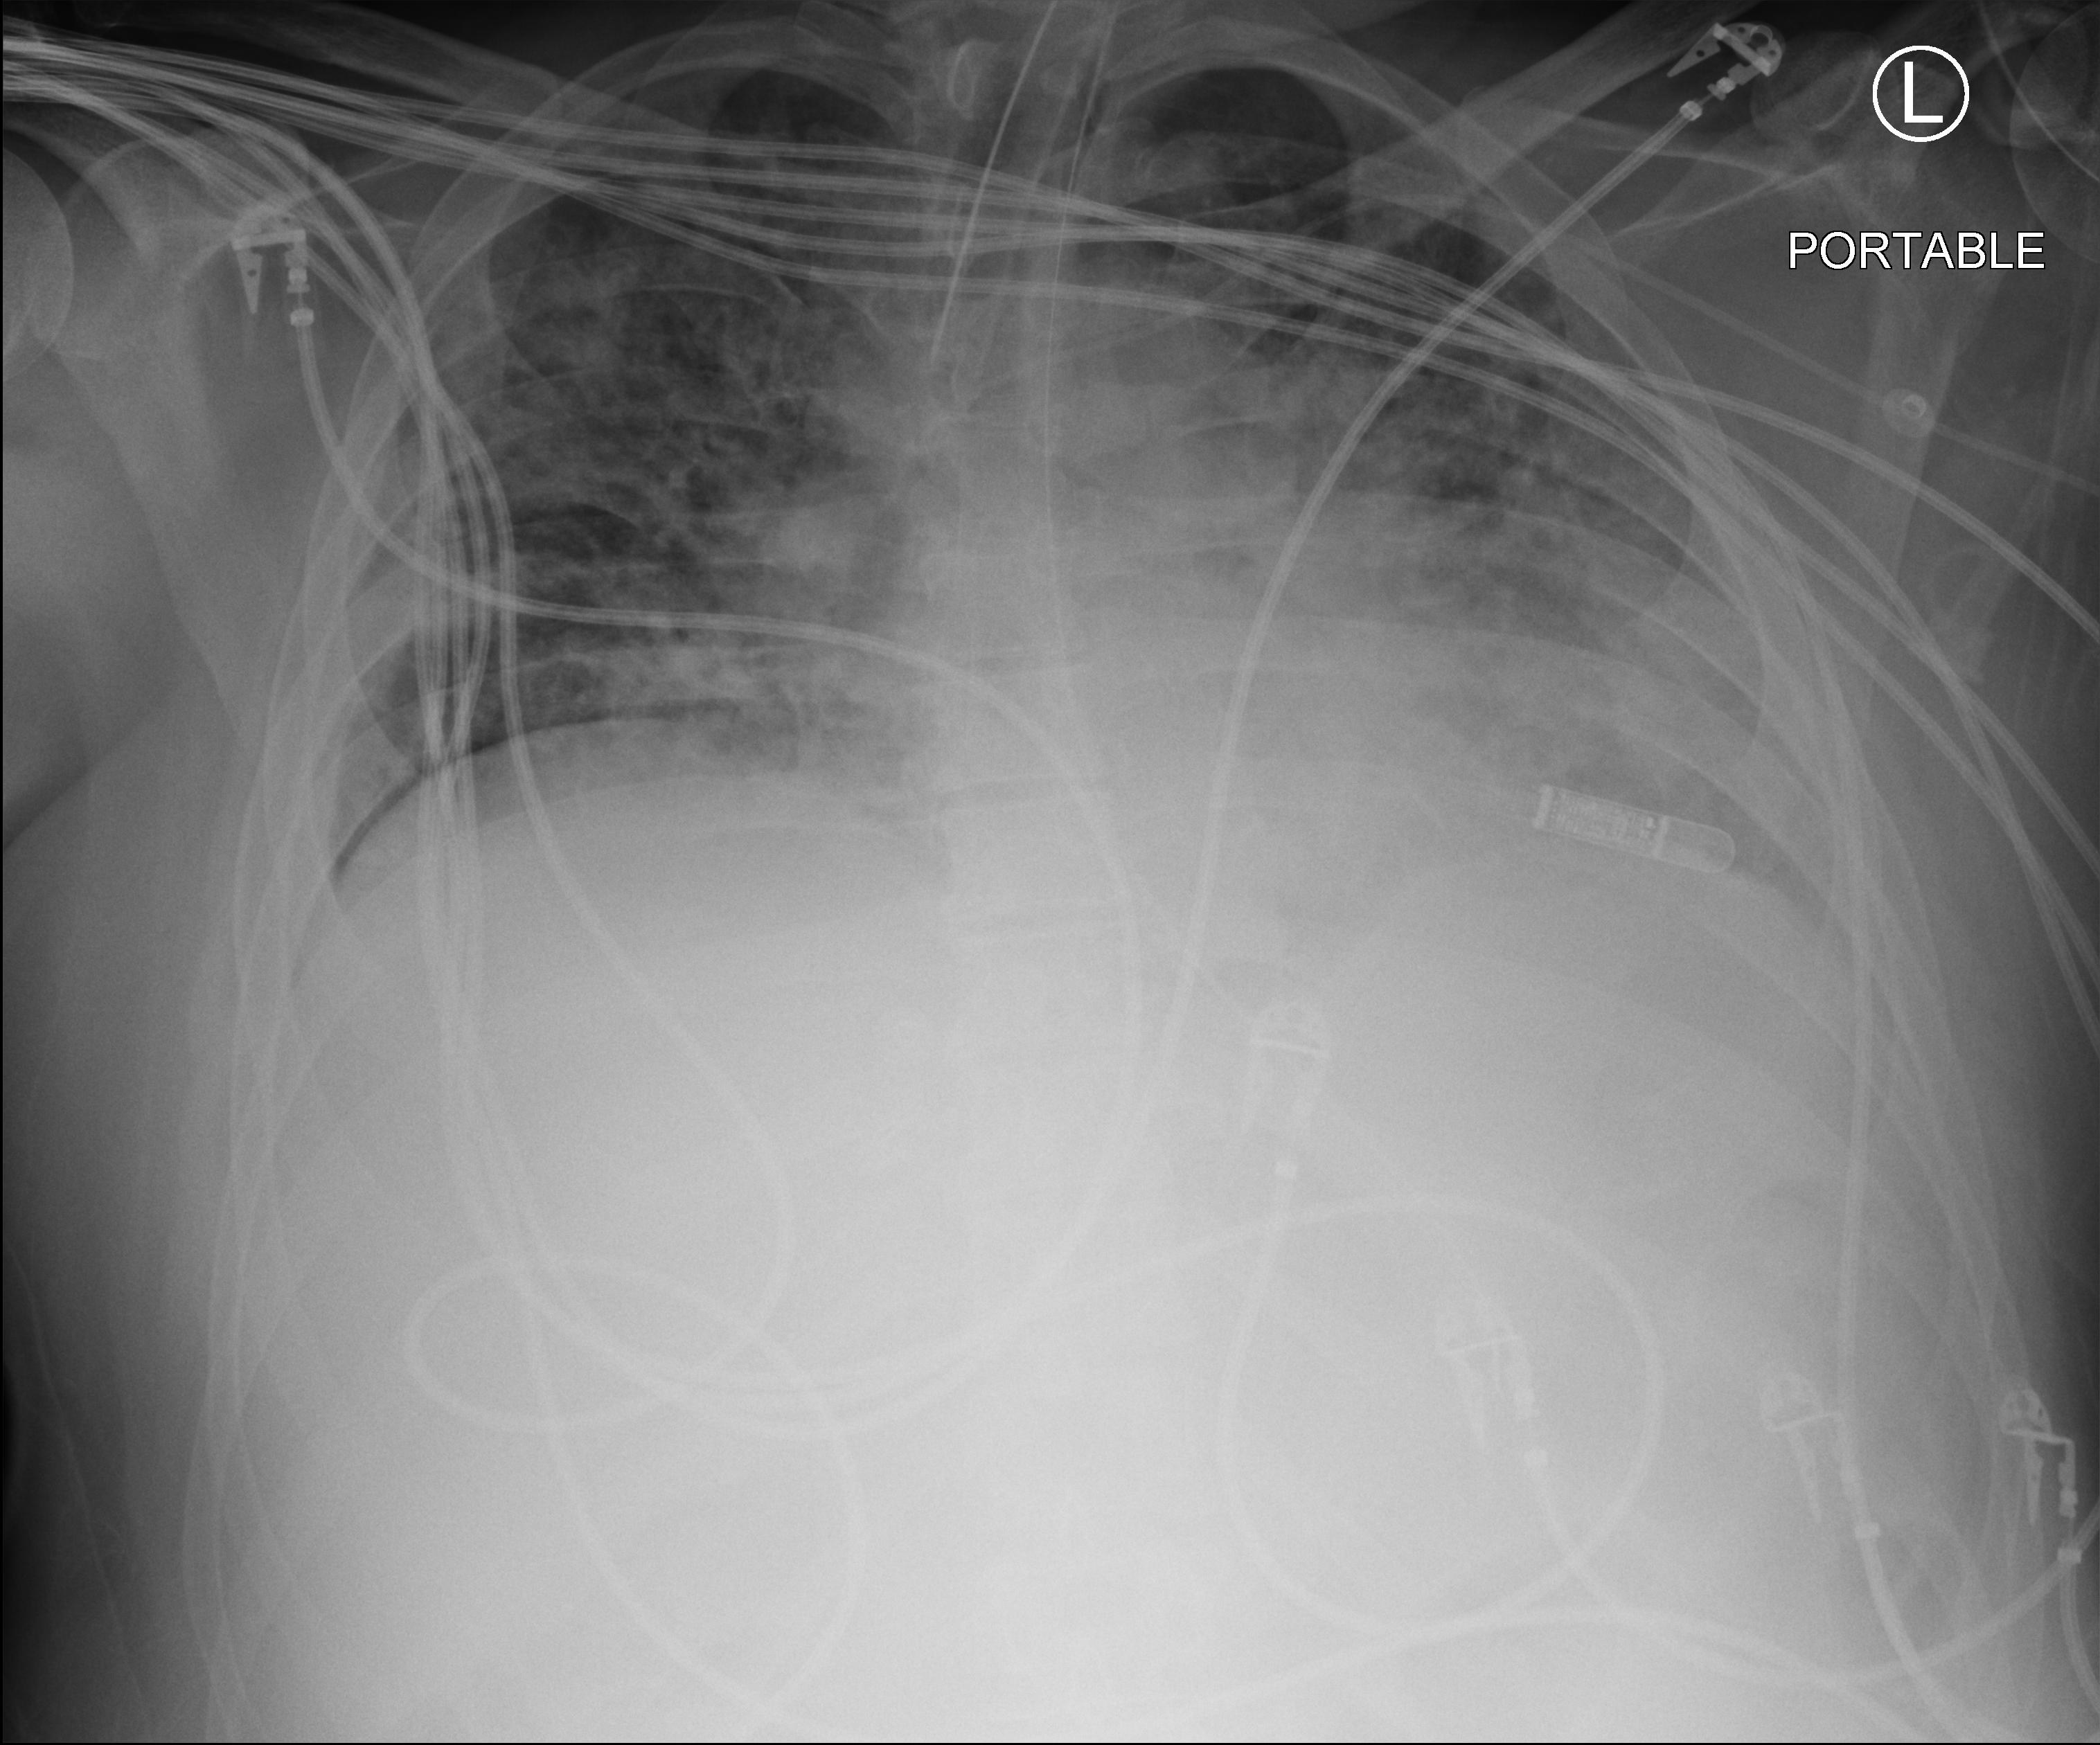
Bedside chest radiograph (computed radiography), anteroposterior (AP) projection. Patient hospitalised with COVID-19; male, aged 18–59 years.
Hospital-stay facts (about this admission, not read from this image; timing relative to this image not recorded): length of hospital stay: 39 days; diabetes (admission record): no.